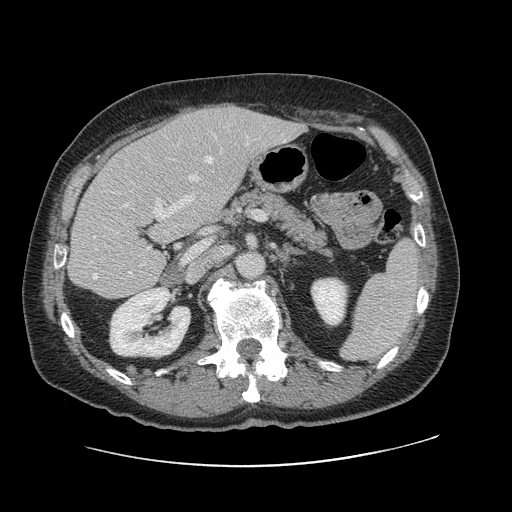
Contrast-enhanced abdominal CT, one axial slice. Position 59 of 138 along the scan axis. 120 kVp. Intravenous contrast given. Soft-tissue window (W 400 / L 40 HU). 2.5 mm slice thickness. 512 × 512 image matrix, field of view 402 × 402 mm. Male patient, age 71 years. Case-level facts recorded for this patient, not image findings: diagnosis: colorectal cancer liver metastases, imaged before liver resection; multiple liver metastases: no; largest metastasis: 3.3 cm; disease in both lobes: no.
Structures marked on this image (manually delineated by an expert):
- hepatic veins: bounding box (x1, y1, x2, y2) in pixels: (93, 156, 227, 279)
- liver: (71, 105, 303, 298)
- planned liver remnant (the part of the liver to remain after resection): (71, 144, 202, 298)
- portal vein (with intrahepatic branches): (96, 143, 249, 250)